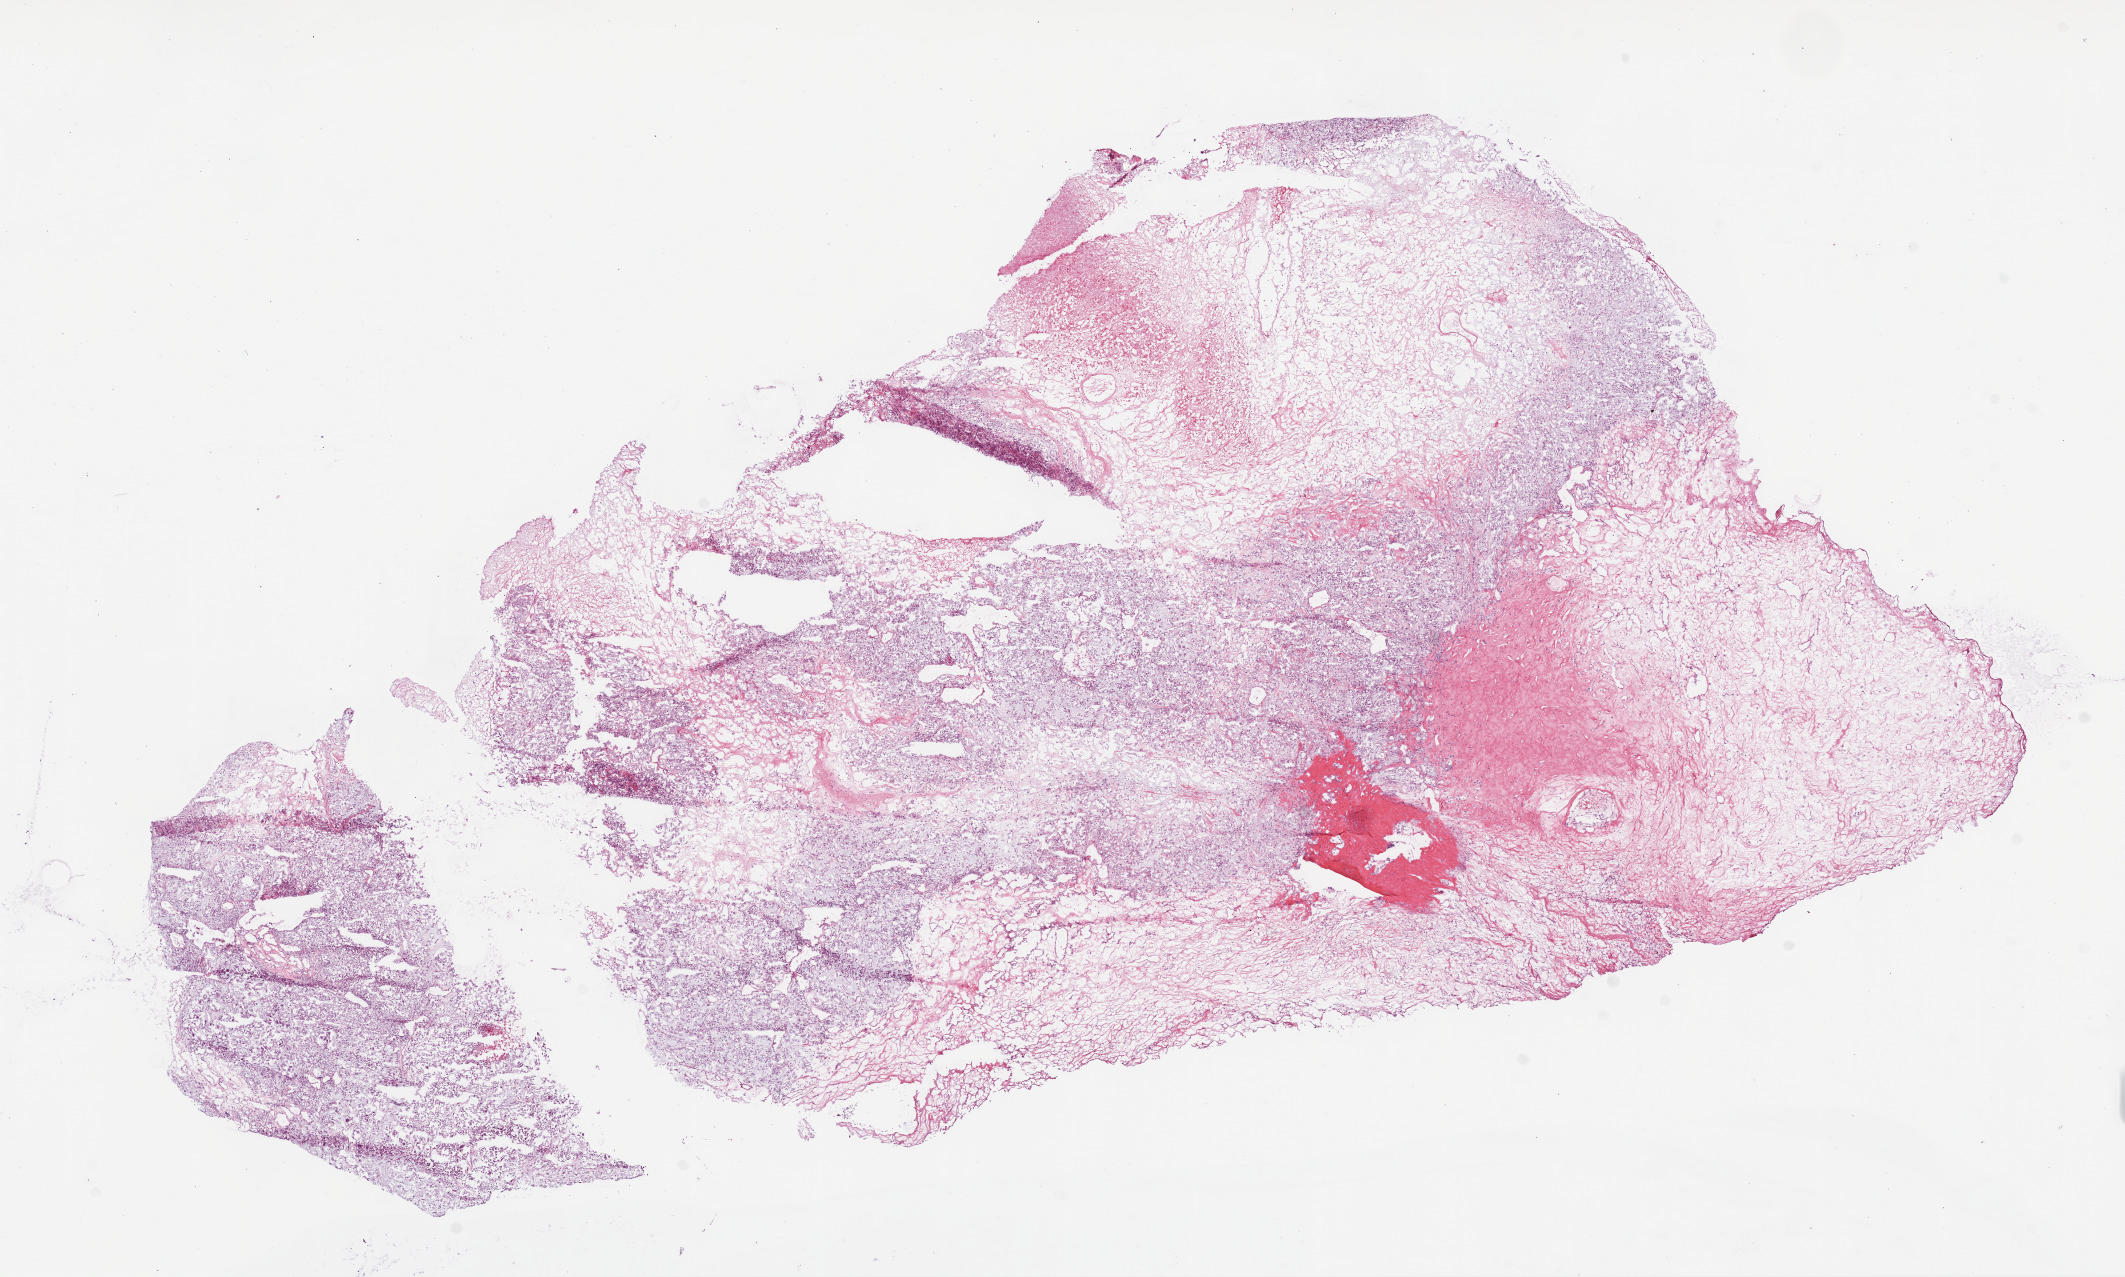
Whole-slide histology image, H&E-stained — a low-resolution overview of the entire scanned area, about 17.1 x 10.2 mm; frozen section from the top of the tissue portion; primary tumour sample from the kidney. Patient: female, age at initial diagnosis 72 years. Histologic grade: GX (grade cannot be assessed). Slide review estimates, as recorded: tumour cells 45%, tumour nuclei 75%, normal cells 0%, stromal cells 50%, necrosis 5%.
Histologic diagnosis: Clear cell adenocarcinoma, NOS. Lymph nodes positive (case pathology): 1 of 1 examined. AJCC pathologic stage: III.